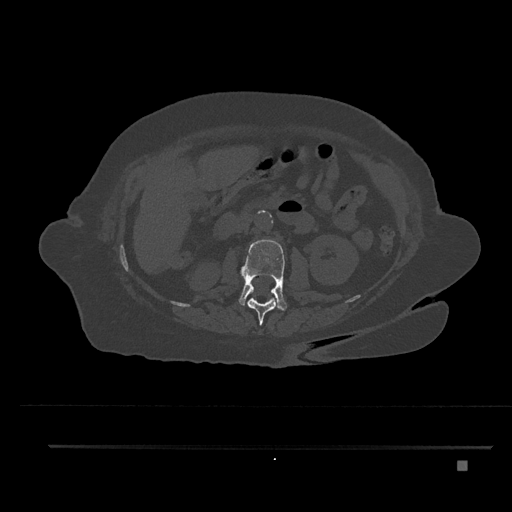
CT including the spine, one axial slice; reconstruction kernel Br40s/3; 120 kVp; bone window (W 1800 / L 400 HU); 0.5 mm slice thickness; 512 × 512 image matrix, field of view 437 × 437 mm. Patient: female, 76 years. From the clinical record (not read from this slice): primary cancer: lung; vertebrae with lytic lesions (as recorded): T11, L3.
Annotated regions visible in this slice (semi-automatically segmented with operator editing):
- L1 vertebra: bounding box <247,298,278,325> (left, top, right, bottom; pixels)
- L2 vertebra: <239,239,287,311>